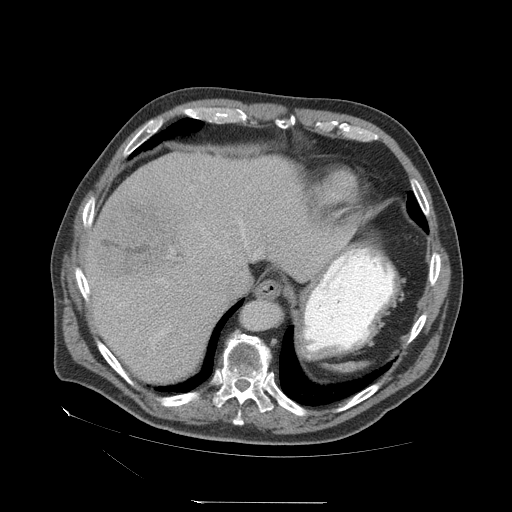
Contrast-enhanced abdominal CT (liver protocol), one axial slice; position 54 of 83 along the scan axis; soft-tissue window (W 400 / L 40 HU); 512 × 512 image matrix, field of view 460 × 460 mm. From the clinical record (not read from this slice): diagnosis: hepatocellular carcinoma (patient treated with transarterial chemoembolisation; whether this scan precedes or follows treatment is not stated here); TNM stage (as recorded): Stage-I; Child-Pugh class: A.
Outlined on this slice (semi-automatically segmented with operator editing):
- liver parenchyma outside the tumour (the mass and vessels are separate outlines, so this box may not span the whole liver): bounding box (x1, y1, x2, y2) in pixels: (84, 152, 351, 382)
- mass: (89, 199, 179, 290)
- liver vessels: (88, 221, 256, 292)